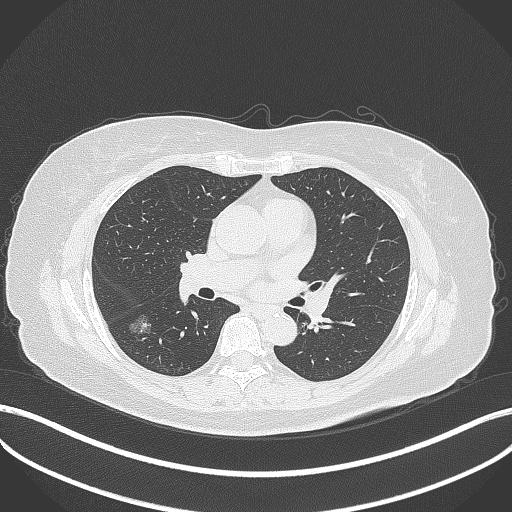
Chest CT, one axial slice; position 173 of 322 along the scan axis; 120 kVp; lung window (W 1500 / L -600 HU); 1 mm slice thickness; 512 × 512 image matrix. Patient: female, 64 years. From the clinical record (not read from this slice): clinical TNM (as recorded): T1c N0 M0; histopathological grade: G1.
Annotated regions visible in this slice (rectangle marked by the reading radiologist):
- lung tumour (recorded histology: adenocarcinoma): bounding box [x1, y1, x2, y2] px = [127, 313, 154, 339]